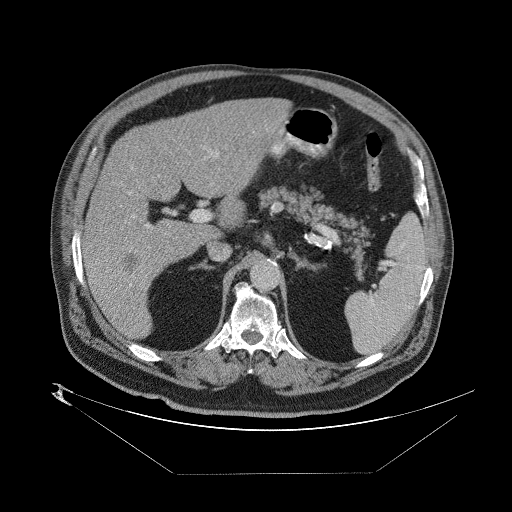
Contrast-enhanced abdominal CT (liver protocol), one axial slice. Position 44 of 89 along the scan axis. One of 2 acquisitions stored at this slice position. Soft-tissue window (W 400 / L 40 HU). 512 × 512 image matrix, field of view 480 × 480 mm. From the clinical record (not read from this slice): diagnosis: hepatocellular carcinoma (patient treated with transarterial chemoembolisation; whether this scan precedes or follows treatment is not stated here); TNM stage (as recorded): Stage-II; Child-Pugh class: B; tumour nodularity: multinodular; tumour size: 4 cm.
Annotated regions visible in this slice (semi-automatically segmented with operator editing):
- abdominal aorta: bounding box [x1, y1, x2, y2] px = [251, 261, 278, 289]
- liver parenchyma outside the tumour (the mass and vessels are separate outlines, so this box may not span the whole liver): [82, 96, 280, 339]
- mass: [117, 250, 142, 270]
- liver vessels: [85, 142, 269, 306]